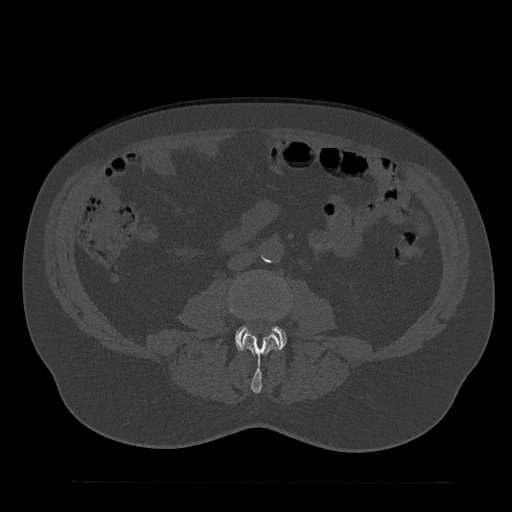
CT including the spine, one axial slice. Slice 4 of 797 in the series (ordered by position). Reconstruction kernel Br40s/3. Bone window (W 1800 / L 400 HU). 0.5 mm slice thickness. 512 × 512 image matrix, field of view 430 × 430 mm. Patient: male, 61 years. From the clinical record (not read from this slice): primary cancer: prostate.
Outlined on this slice (semi-automatic segmentation, software-assisted and operator-edited):
- L3 vertebra: bounding box <230,303,279,393> (left, top, right, bottom; pixels)
- L4 vertebra: <235,326,286,350>